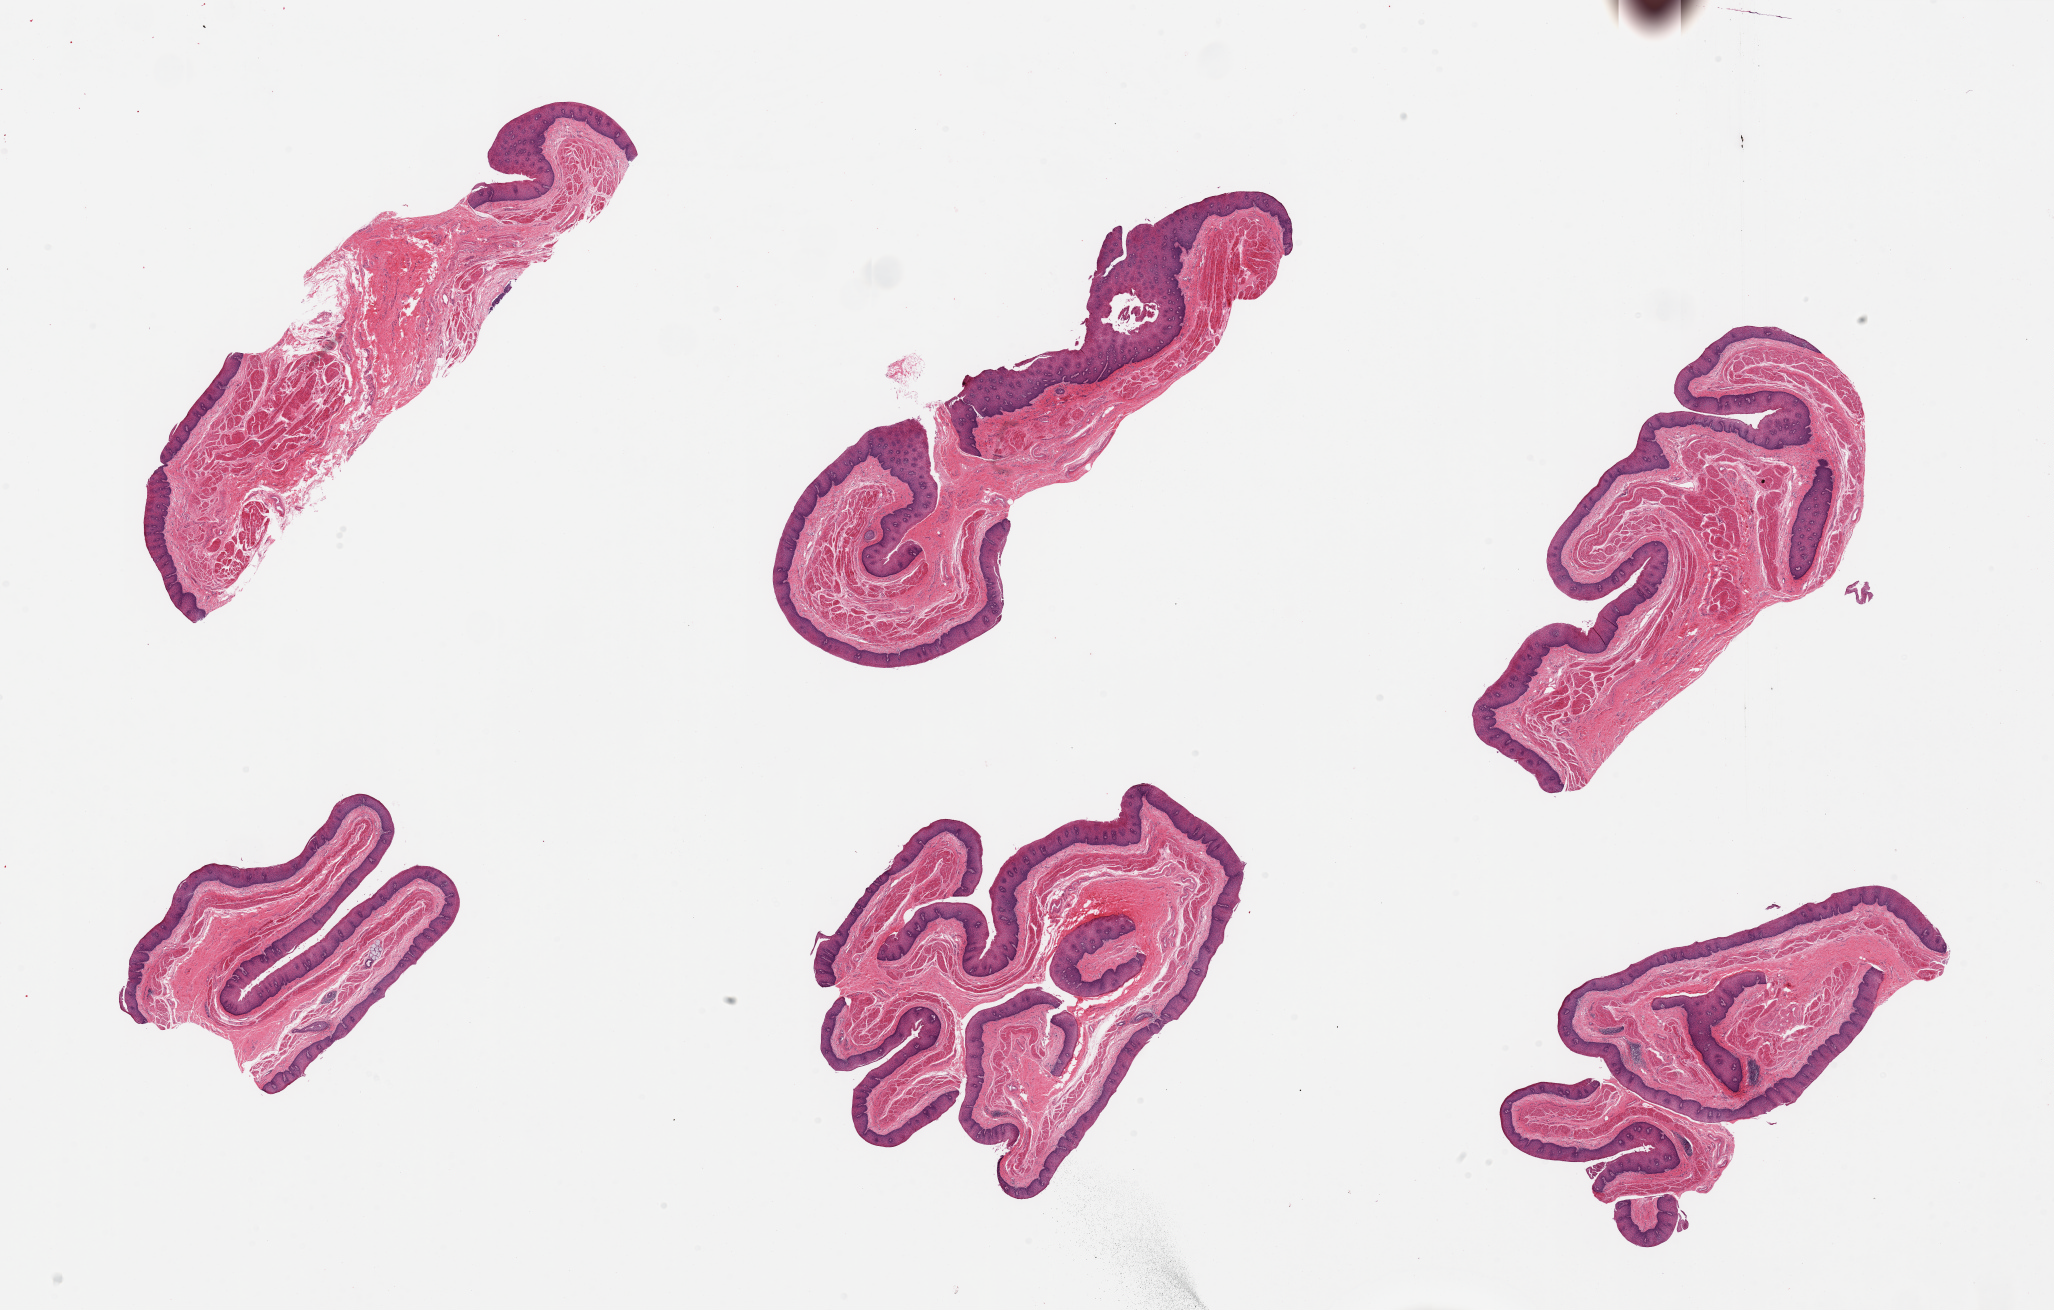
Digitized H&E-stained section, low-resolution overview of the scanned area, about 32.5 x 20.7 mm, PAXgene-fixed, paraffin-embedded tissue, target tissue: esophageal mucous membrane, tissue donor sample. Donor sex: male.
* reviewer comment on this tissue sample: 6 pieces, squamous mucosa is ~0.25mm, ~10-15% total thickness